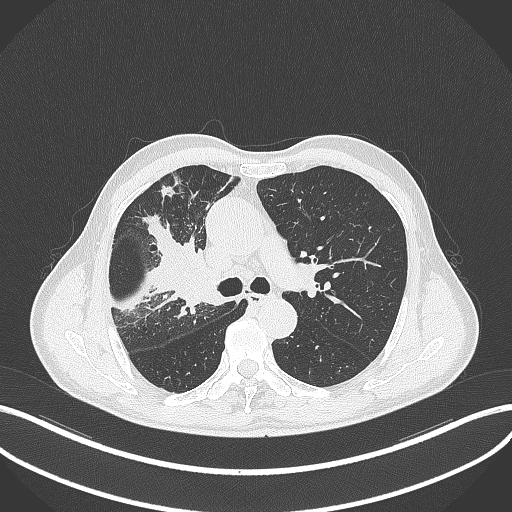
Chest CT, one axial slice. Position 317 of 490 along the scan axis. Reconstruction kernel B70f. Lung window (W 1500 / L -600 HU). 1 mm slice thickness. 512 × 512 image matrix, field of view 400 × 400 mm. Patient: male, 69 years. From the clinical record (not read from this slice): clinical TNM (as recorded): T2a N0 M0.
Annotated regions visible in this slice (rectangle marked by the reading radiologist):
- lung tumour (recorded histology: adenocarcinoma): bounding box [x1, y1, x2, y2] px = [161, 241, 223, 316]